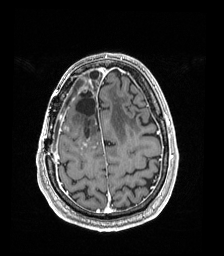
Brain MRI from a brain-tumour surgery series, one axial slice; slice 47 of 192 in the series (ordered by position); T1-weighted post-contrast; 224 × 256 image matrix, field of view 224 × 256 mm. From the clinical record (not read from this slice): histopathology: Astrocytoma; WHO grade: 4; IDH mutation: yes.
Structures marked on this image (outlined manually by an expert reader):
- previous resection cavity: bounding box (x1, y1, x2, y2) in pixels: (76, 91, 97, 118)
- tumour: (85, 84, 87, 91)